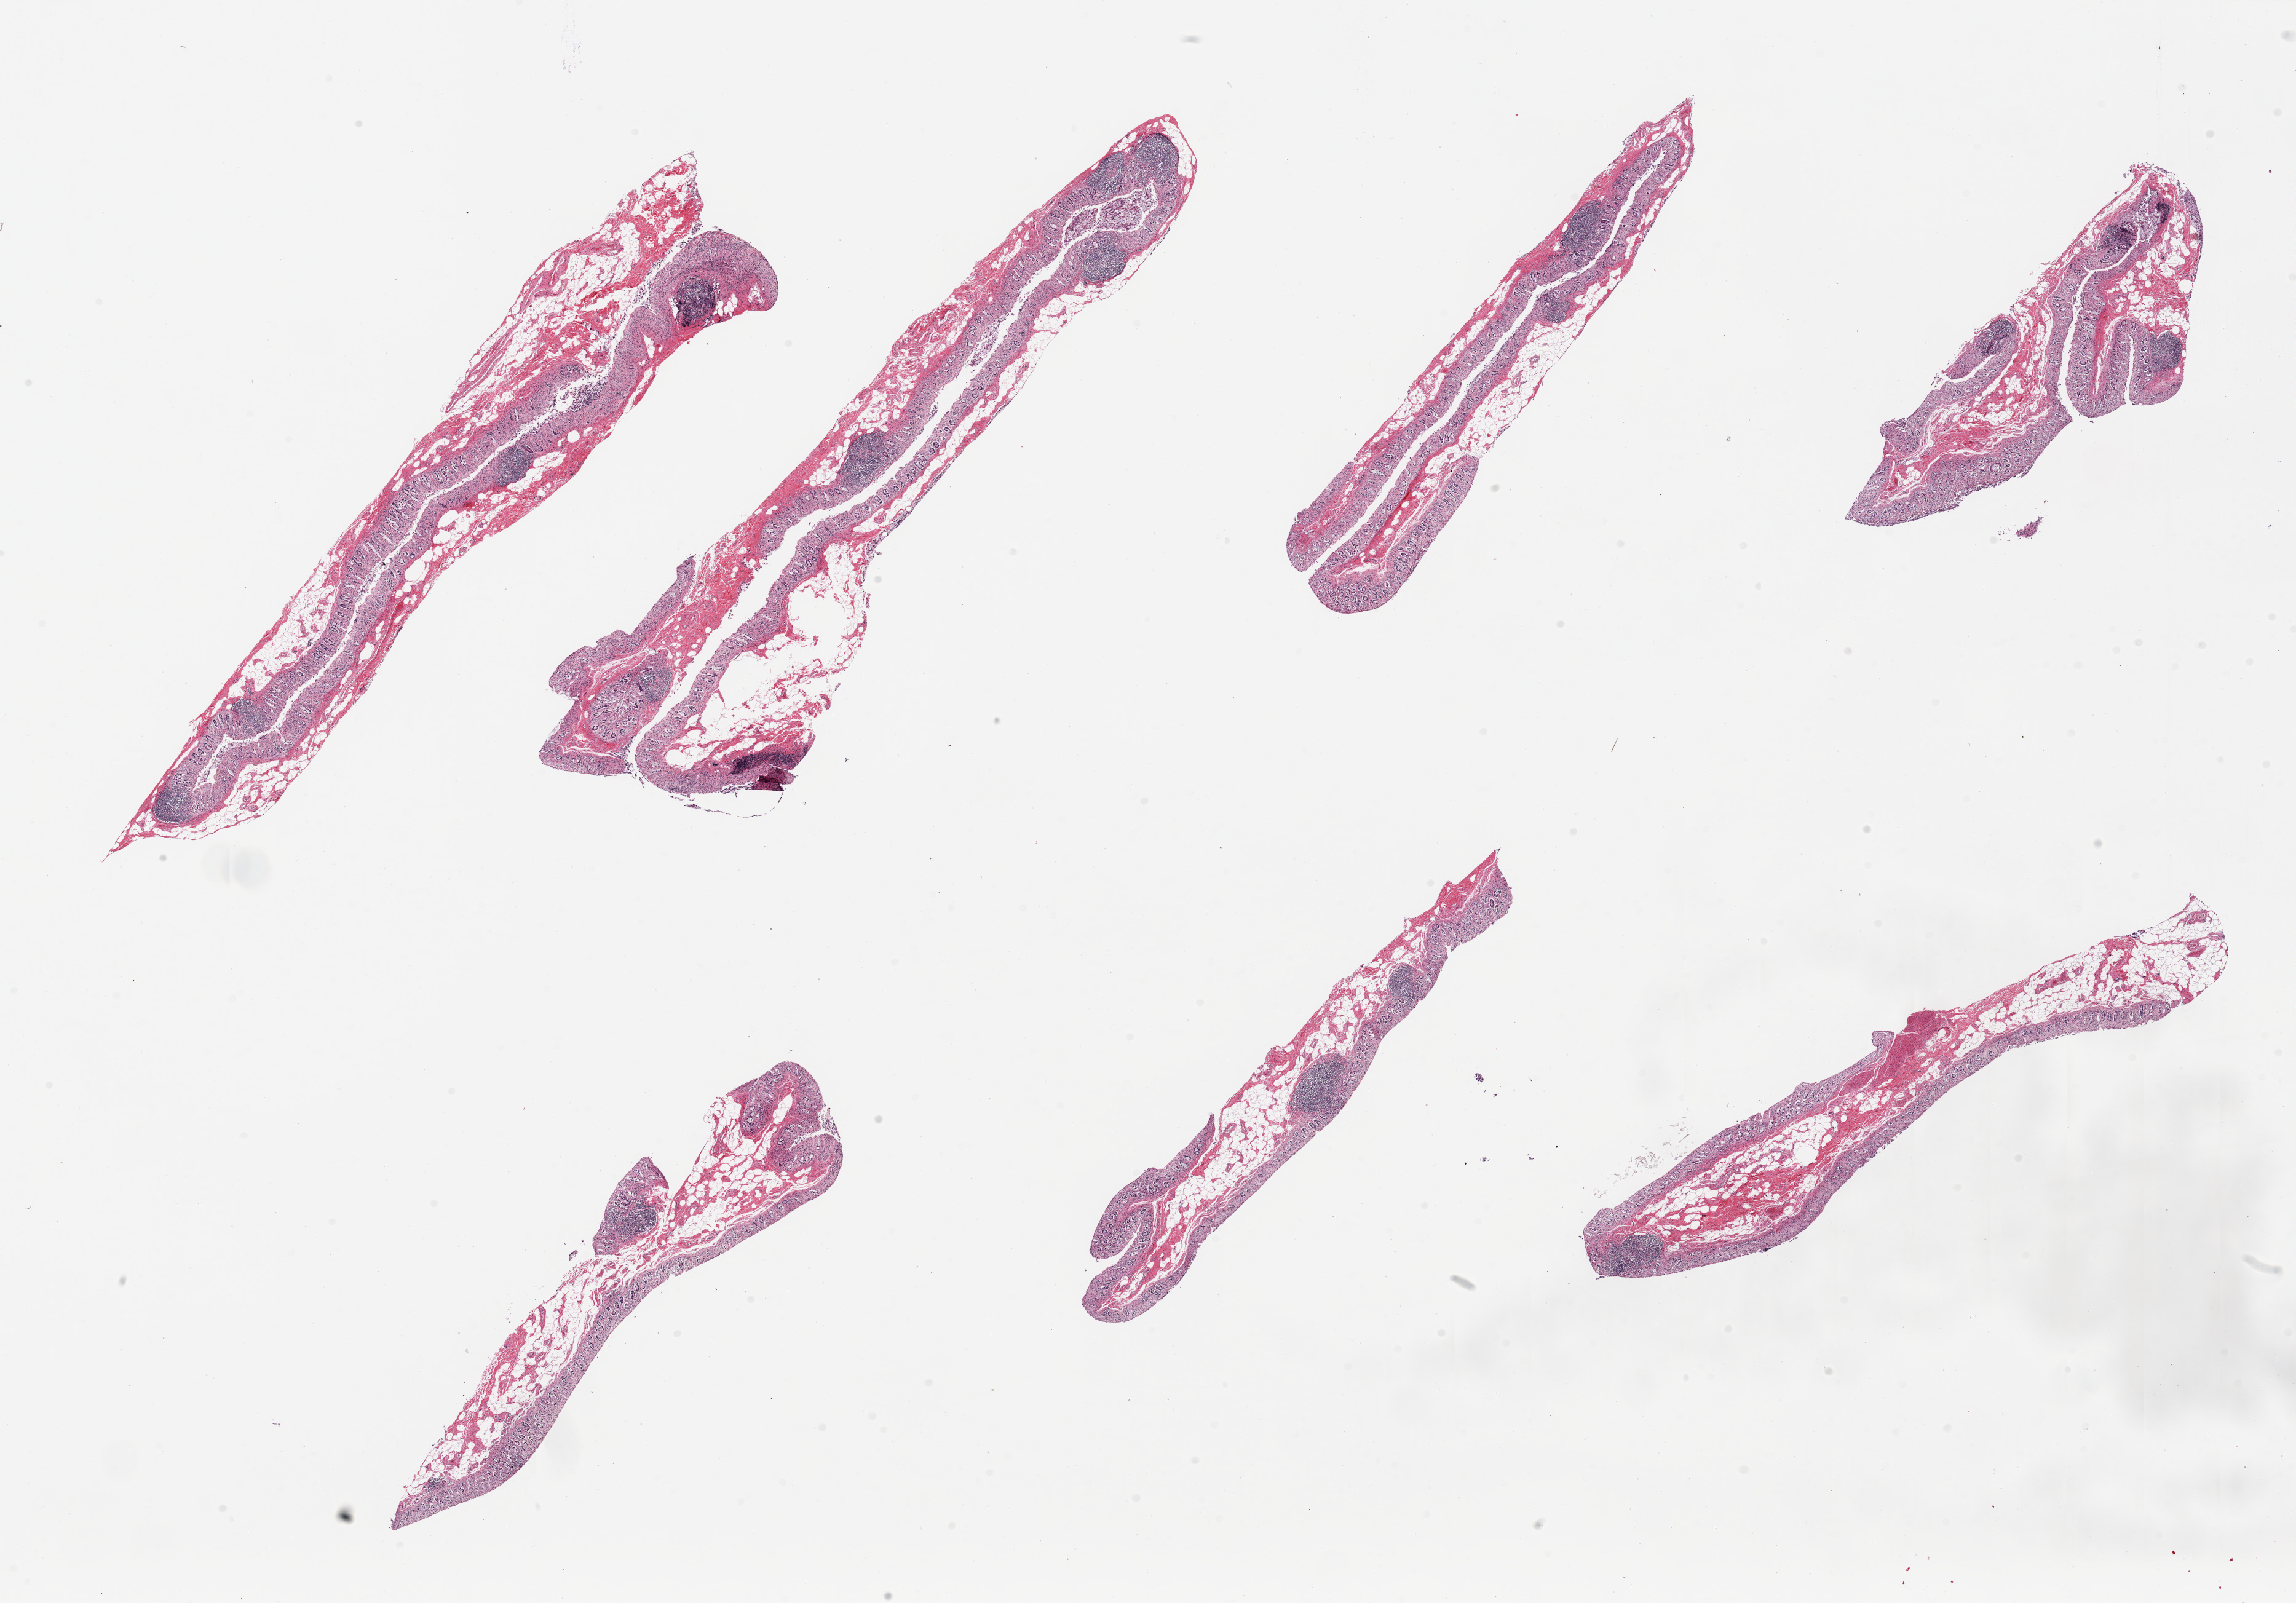
Whole-slide image, H&E stain, brightfield, a low-resolution overview of the entire scanned area, about 29.5 x 20.6 mm (acquisition: 20x scan), PAXgene-fixed paraffin-embedded (PFPE) section, section of transverse colon (target tissue), donor tissue sample. Donor sex: male.
Review note (as recorded): 6 pieces, mucosa with advanced autolysis/sloughed.